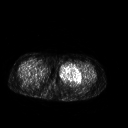
FDG PET of an extremity soft-tissue mass (from a PET/CT study), one axial slice. Position 241 of 267 along the scan axis. 128 × 128 image matrix. Patient: female, 42 years. From the clinical record (not read from this slice): histological type: pleiomorphic leiomyosarcoma; grade: intermediate; site of the primary tumour: left thigh.
Annotated regions visible in this slice (expert contour drawn on MRI and transferred to this co-registered scan by the dataset authors):
- gross tumour volume including surrounding oedema: bounding box (x1, y1, x2, y2) in pixels: (59, 64, 82, 83)
- gross tumour volume (mass): (59, 64, 82, 83)